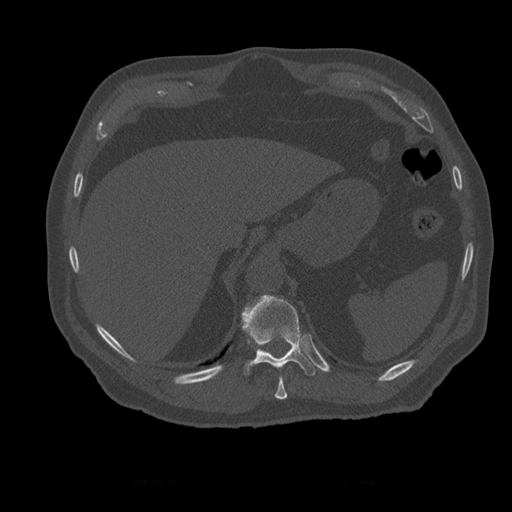
CT including the spine, one axial slice. Slice 283 of 399 in the series (ordered by position). Bone window (W 1800 / L 400 HU). 512 × 512 image matrix. Patient age 73 years. Case-level facts recorded for this patient, not image findings: primary cancer: prostate; vertebrae with lytic lesions (as recorded): L2.
Structures marked on this image (semi-automatic segmentation, software-assisted and operator-edited):
- T10 vertebra: box from (x=275, y=377) to (x=288, y=400) px
- T11 vertebra: (x=242, y=295)–(x=316, y=376)
- T12 vertebra: (x=246, y=306)–(x=253, y=309)